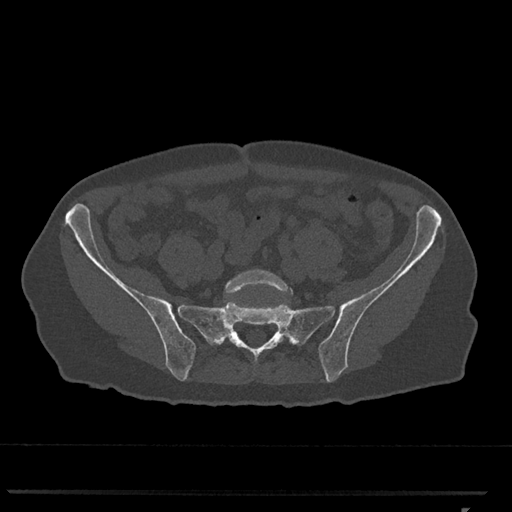
CT including the spine, one axial slice. Position 113 of 793 along the scan axis. Reconstruction kernel Br40s/3. Bone window (W 1800 / L 400 HU). 0.5 mm slice thickness. 512 × 512 image matrix. Patient: female, 62 years. From the clinical record (not read from this slice): primary cancer: renal.
Structures marked on this image (semi-automatically segmented with operator editing):
- L5 vertebra: bounding box (x1, y1, x2, y2) in pixels: (225, 269, 293, 339)